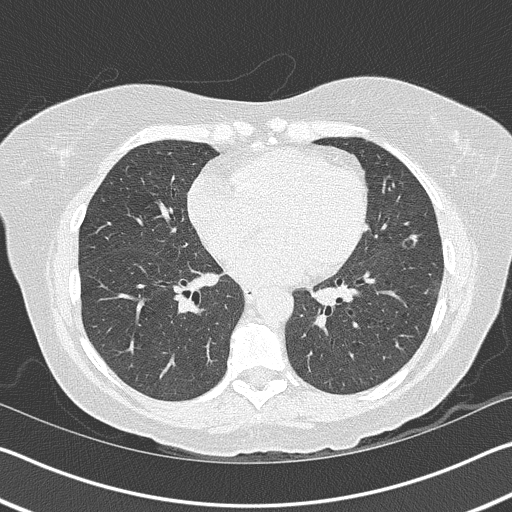
Low-dose screening chest CT, axial slice, baseline screening round, lung window (W 1500 / L -600 HU), 2 mm slice thickness, lung (sharp) reconstruction kernel (B50f), slice 71 of 157 in the series, 512 × 512 image matrix. Female participant, aged 63 years at enrolment. Current smoker at enrolment.
- Lesion marked by an expert reader, bounding box <386,220,438,260> (left, top, right, bottom; pixels).
- The screening reader recorded 3 non-calcified nodules or masses ≥4 mm on this exam (right upper lobe, left upper lobe, lingula); which of them this box marks is not recorded.